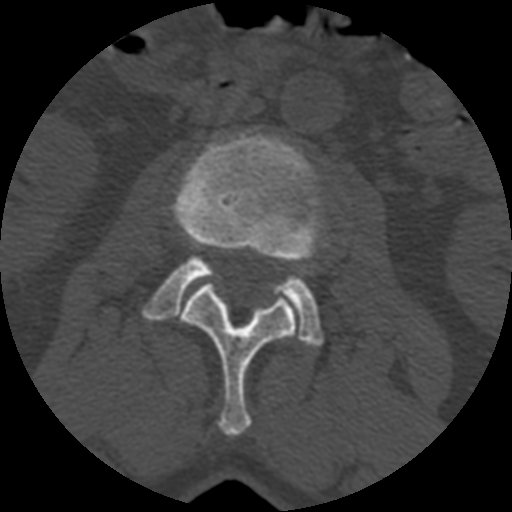
CT including the spine, one axial slice; position 321 of 399 along the scan axis; reconstruction kernel STANDARD; bone window (W 1800 / L 400 HU); 1.25 mm slice thickness; 512 × 512 image matrix, field of view 160 × 160 mm. Patient age 71 years. From the clinical record (not read from this slice): primary cancer: prostate.
Structures marked on this image (semi-automatically segmented with operator editing):
- L2 vertebra: bounding box <174,282,295,436> (left, top, right, bottom; pixels)
- L3 vertebra: <142,131,326,346>